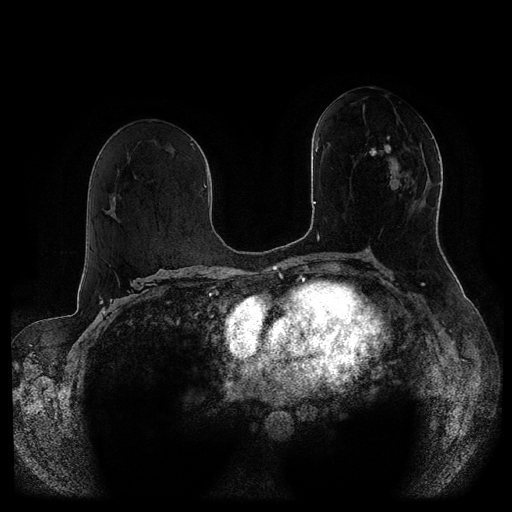
Breast MRI (dynamic contrast-enhanced, multi-phase), one axial slice. Position 50 of 116 along the scan axis. Dynamic contrast-enhanced series, time point 2 of 5 at this slice position (early post-contrast). 1.5 T. TE 2.6 ms, TR 5.3 ms. 2 mm slice thickness. 512 × 512 image matrix, field of view 370 × 370 mm. Female patient, age 51 years.
Annotated regions visible in this slice (semi-automatically segmented with operator editing):
- breast lesion (labelled 'tumour' in the annotation; benign lesions carry a separate 'benign' label): bounding box [x1, y1, x2, y2] px = [365, 136, 414, 193]